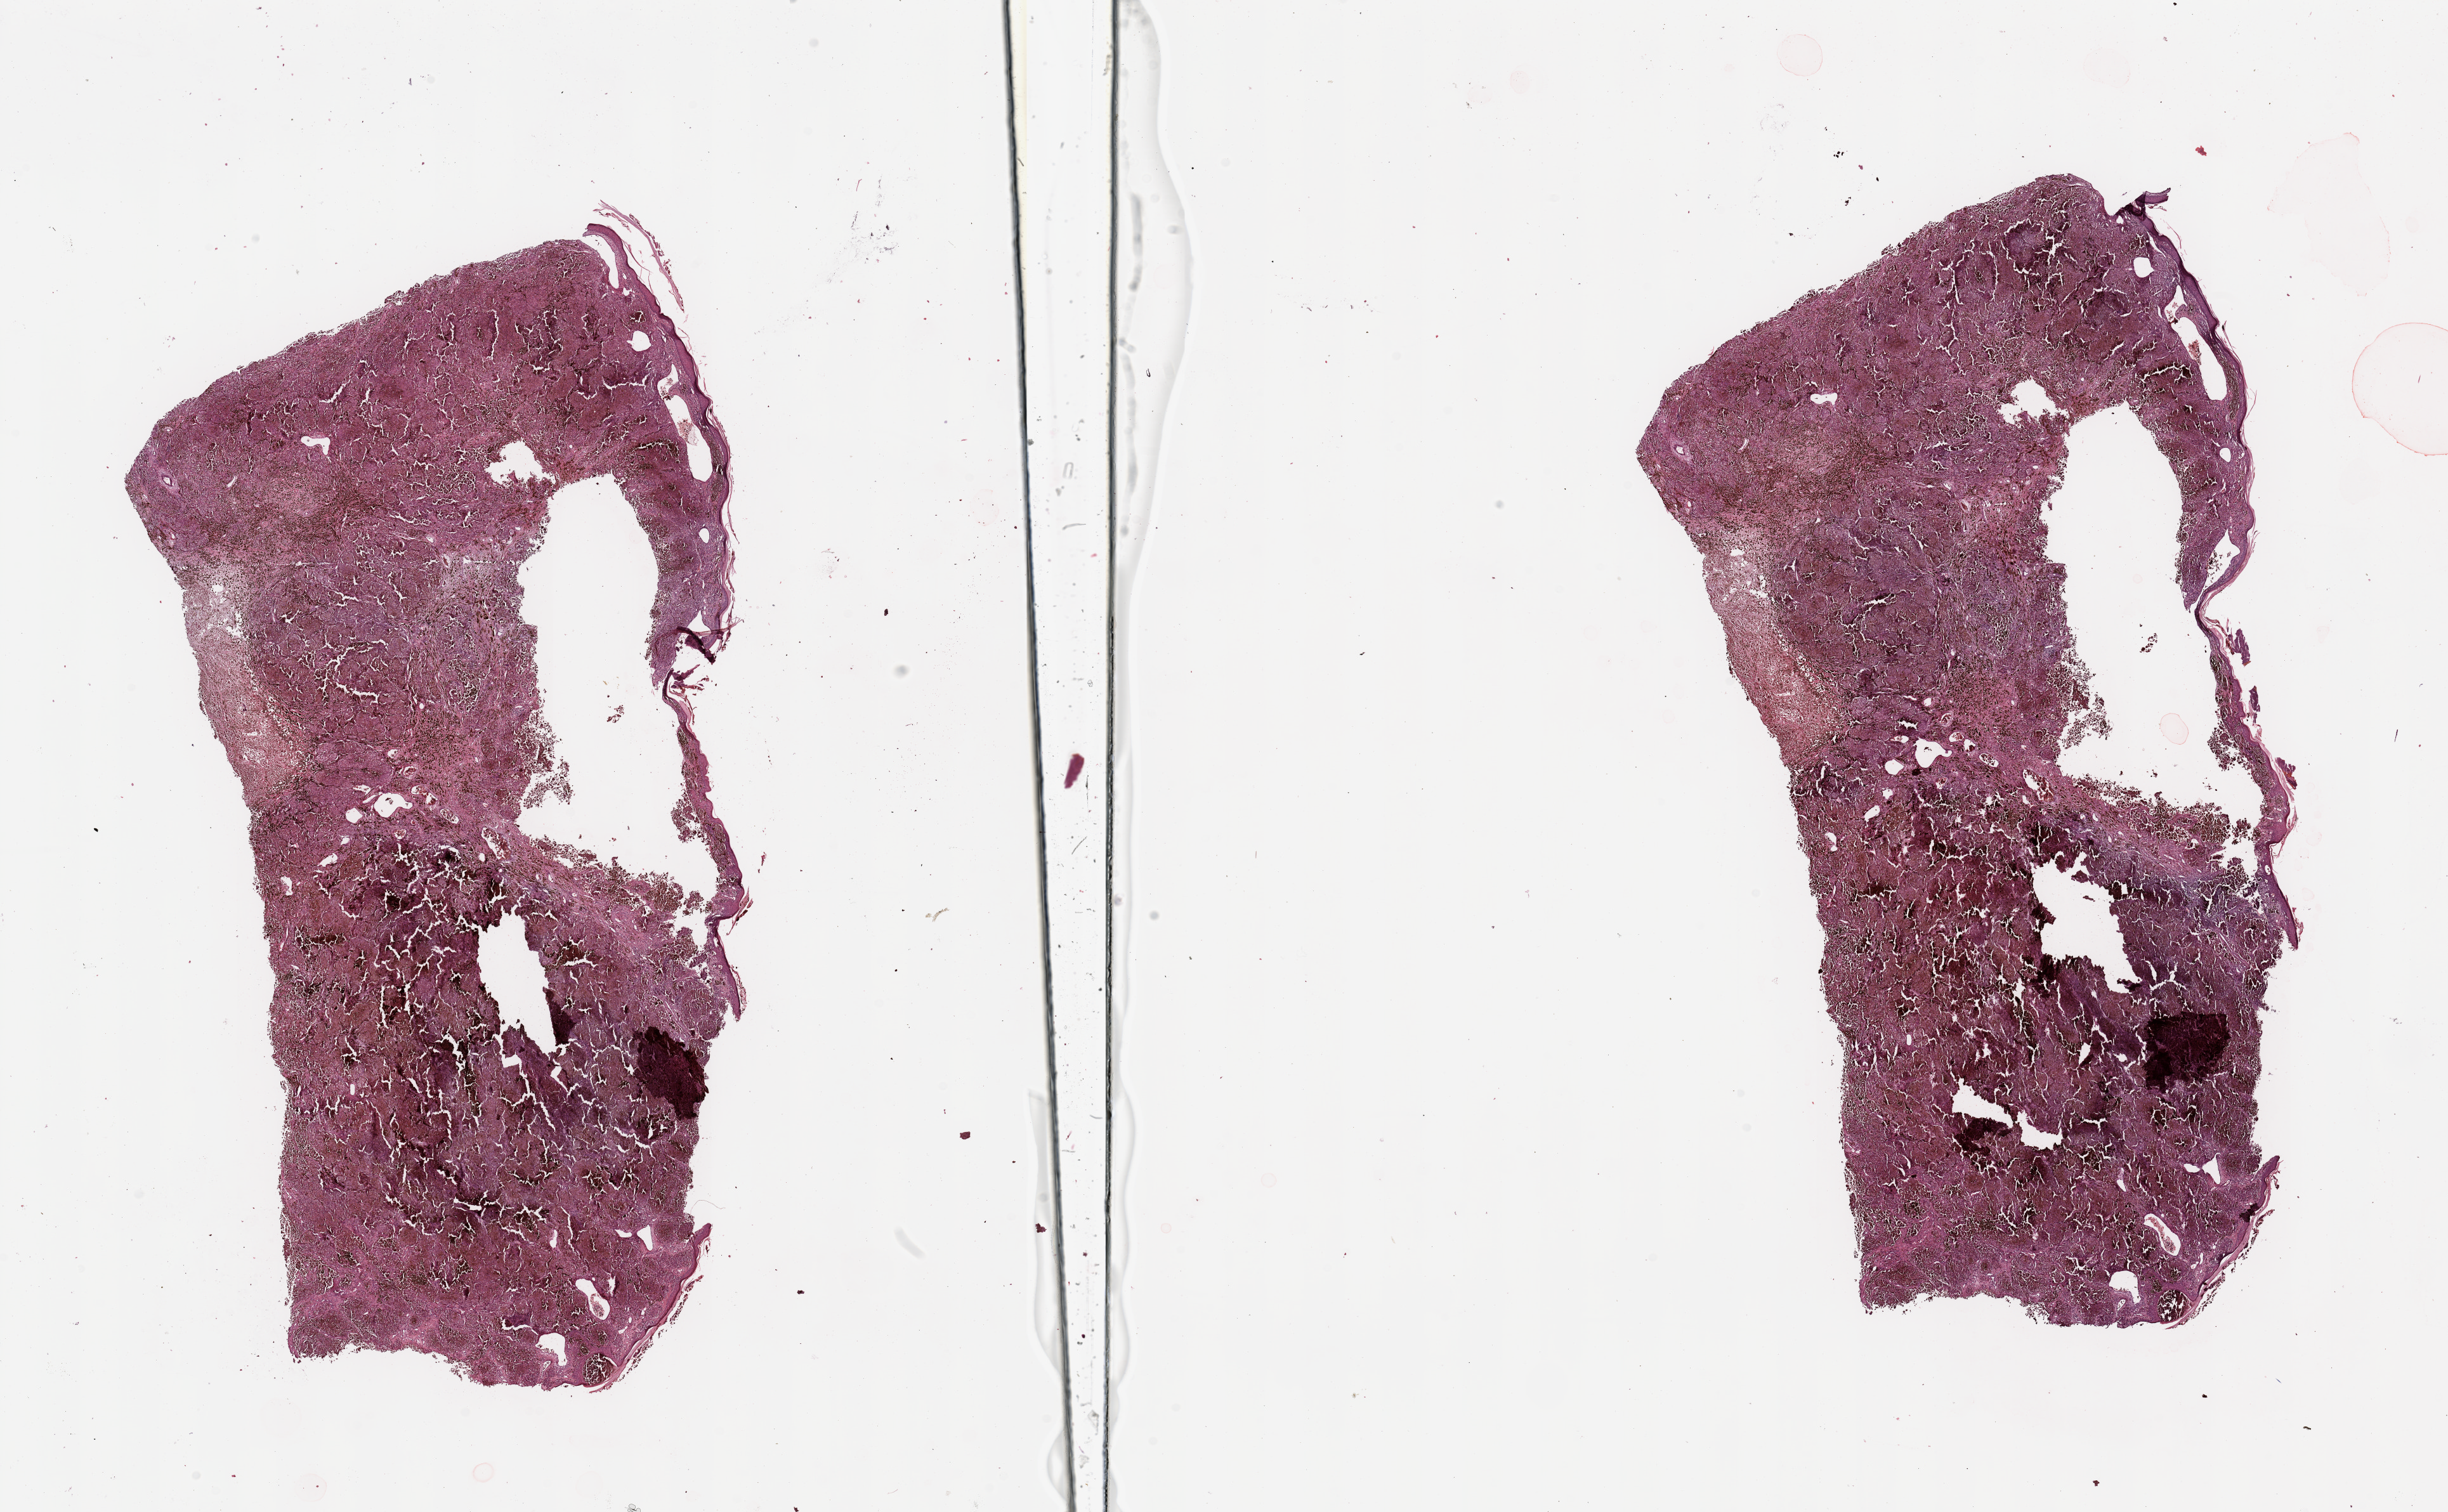
Hematoxylin and eosin (H&E) stained whole-slide image, whole scanned area (about 30.5 x 18.9 mm) shown as a low-resolution overview, tumour tissue sample, sampled site: trunk. Patient: male, age 66 years. Slide review estimates, as recorded: tumour nuclei 98%, necrosis 0%.
Diagnosis: Malignant melanoma, NOS. AJCC pathologic stage: IV. Primary tumour site (as recorded): trunk.